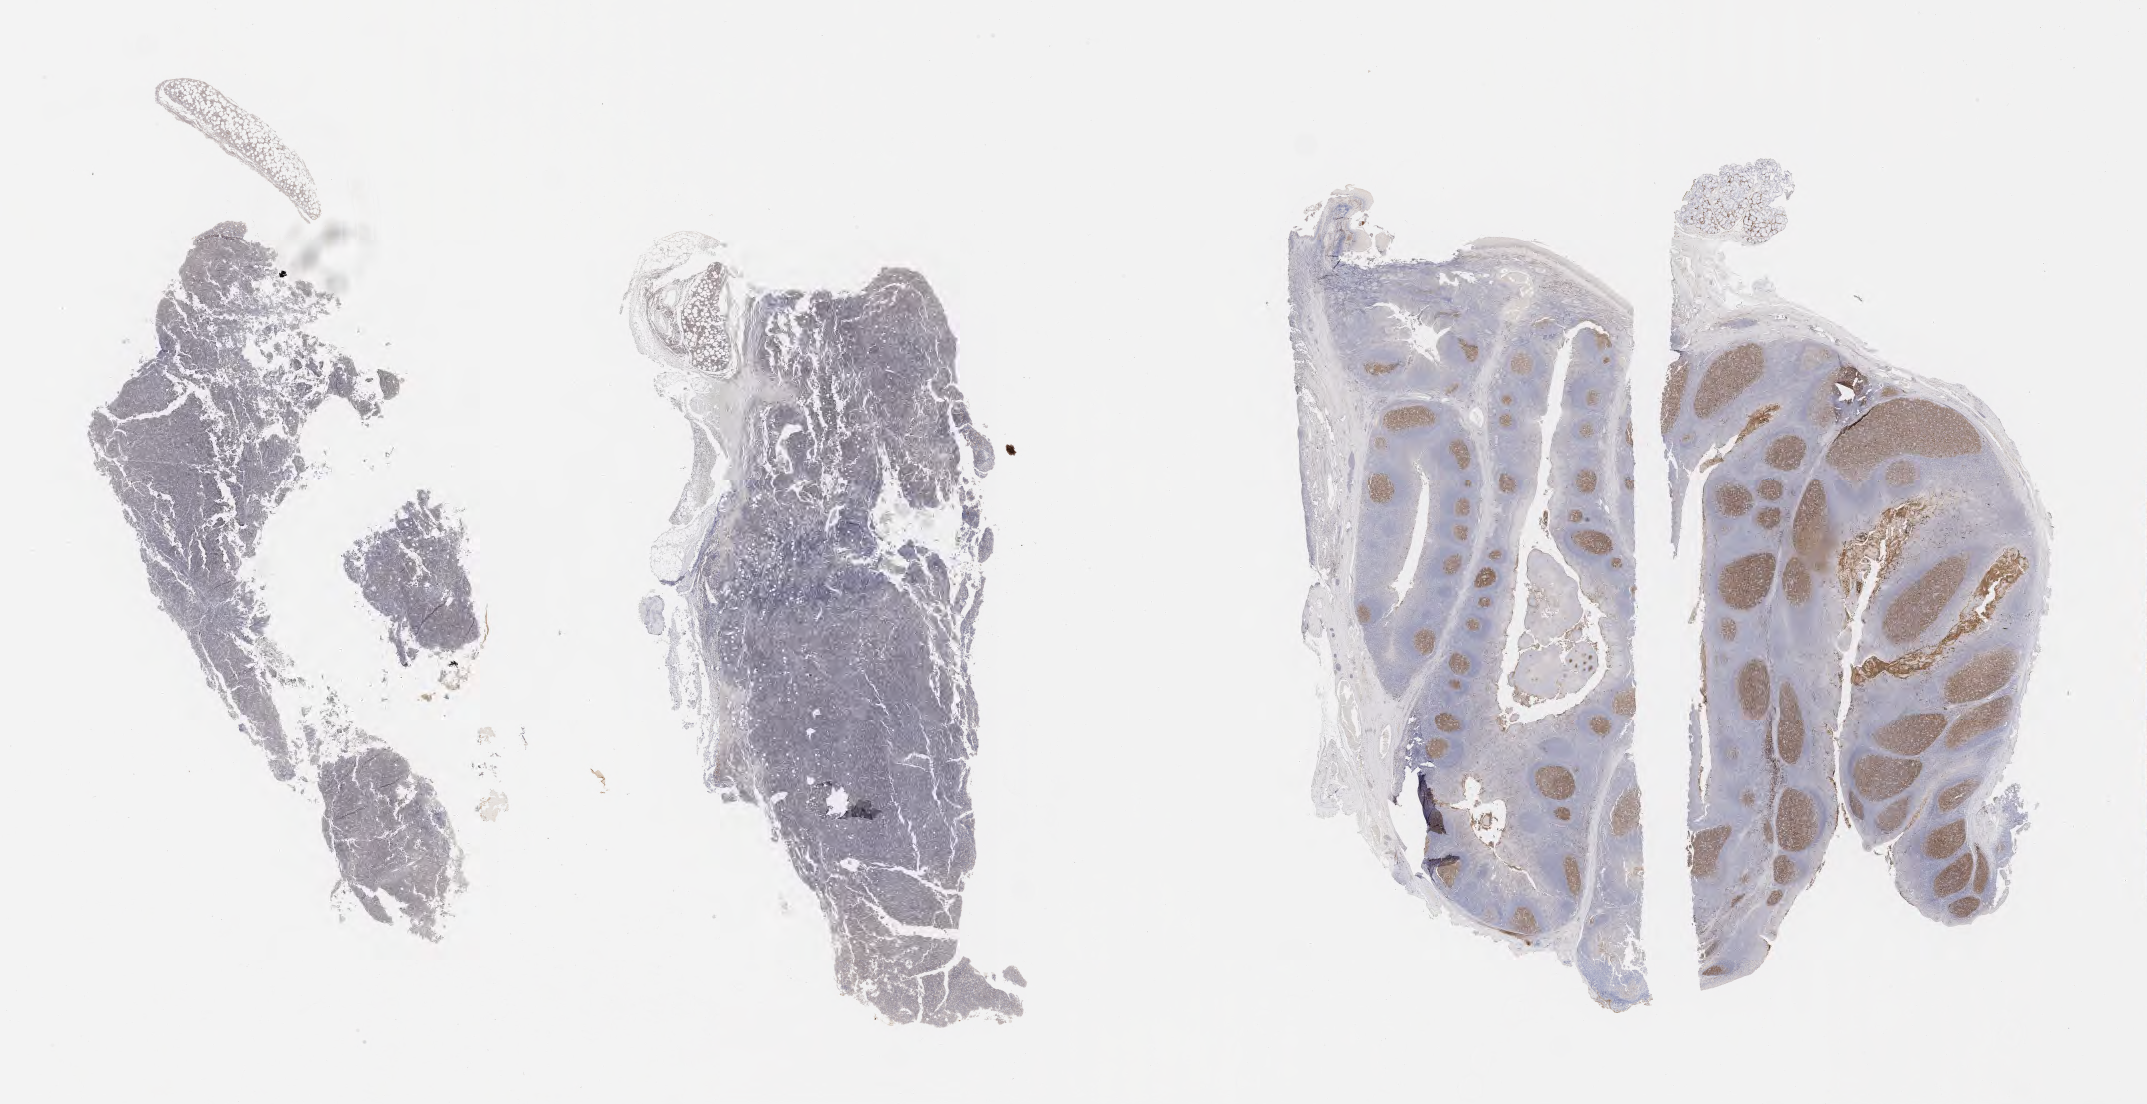
Immunohistochemistry (IHC) whole-slide image stained for CD10, whole scanned area (about 34.7 x 17.9 mm) shown as a low-resolution overview; tumor tissue. Patient female; aged 16.
Histologic diagnosis: Burkitt lymphoma, NOS.